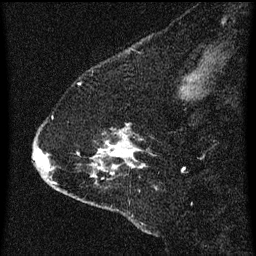
Breast MRI (dynamic contrast-enhanced), one sagittal slice; slice 14 of 60 in the series (ordered by position); dynamic contrast-enhanced series, image 2 of 3 at this slice position (ordered by acquisition); 1.5 T; TE 4.2 ms, TR 8 ms; 2 mm slice thickness; 256 × 256 image matrix, field of view 180 × 180 mm. Female patient, age 47 years.
Annotated regions visible in this slice (semi-automatic segmentation, software-assisted and operator-edited):
- analysis volume of interest (the breast-tissue region the enhancement analysis was run in; not a lesion): box from (x=36, y=118) to (x=152, y=211) px
- tumour enhancement mask (voxels above the 70 % enhancement threshold inside the analysis volume of interest): (x=36, y=124)–(x=132, y=175)